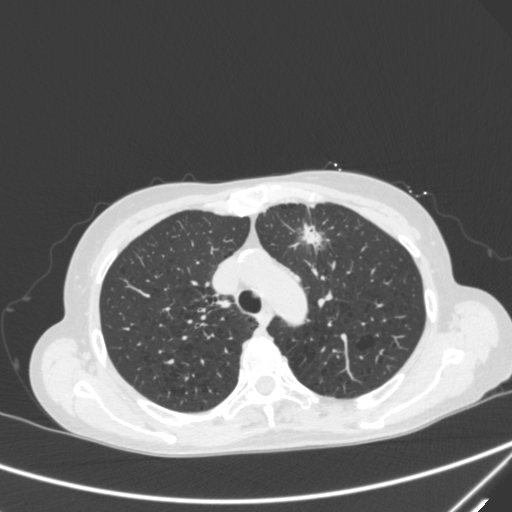
Chest CT, one axial slice; 120 kVp; lung window (W 1500 / L -600 HU); 1 mm slice thickness; 512 × 512 image matrix, field of view 350 × 350 mm. Patient: female, 71 years. From the clinical record (not read from this slice): clinical TNM (as recorded): T1c N0 M0.
Annotated regions visible in this slice (rectangle marked by the reading radiologist):
- lung tumour (recorded histology: adenocarcinoma): bounding box [x1, y1, x2, y2] px = [291, 217, 330, 257]